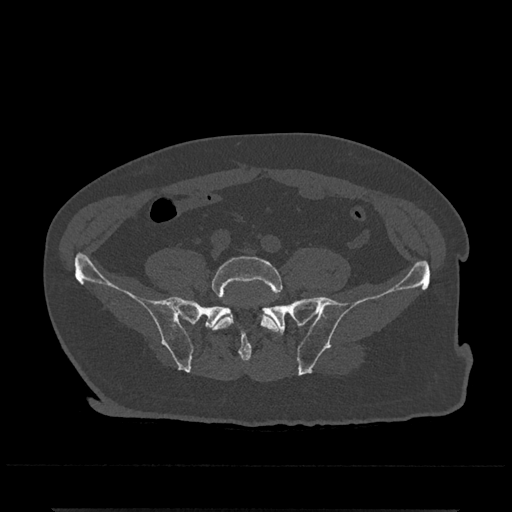
CT including the spine, one axial slice; position 58 of 797 along the scan axis; bone window (W 1800 / L 400 HU); 0.5 mm slice thickness; 512 × 512 image matrix. Male patient, age 67 years. Case-level facts recorded for this patient, not image findings: primary cancer: prostate.
Outlined on this slice (semi-automatic segmentation, software-assisted and operator-edited):
- L5 vertebra: bounding box (x1, y1, x2, y2) in pixels: (209, 256, 282, 332)